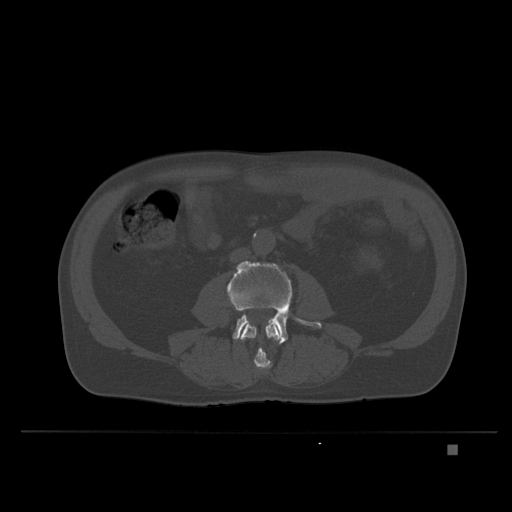
CT including the spine, one axial slice. Position 85 of 435 along the scan axis. Bone window (W 1800 / L 400 HU). 1.5 mm slice thickness. 512 × 512 image matrix, field of view 434 × 434 mm. Patient: male, 73 years. Case-level facts recorded for this patient, not image findings: primary cancer: skin.
Outlined on this slice (semi-automatic segmentation, software-assisted and operator-edited):
- L3 vertebra: bounding box (x1, y1, x2, y2) in pixels: (240, 320, 281, 371)
- L4 vertebra: (227, 260, 322, 345)